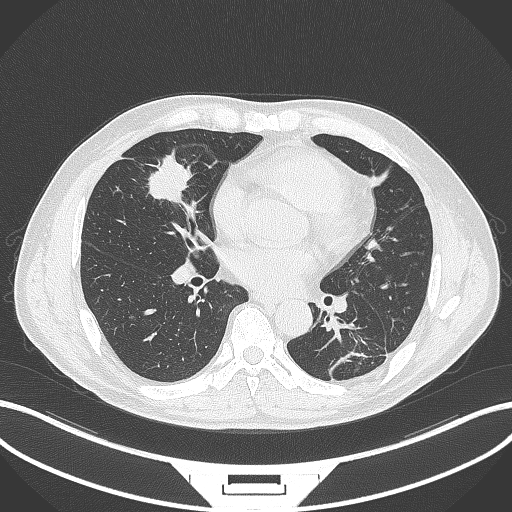
Chest CT, one axial slice; 120 kVp; lung window (W 1500 / L -600 HU); 1 mm slice thickness; 512 × 512 image matrix. Patient: male, 59 years. From the clinical record (not read from this slice): clinical TNM (as recorded): T2a N1 M0.
Outlined on this slice (bounding box drawn by a radiologist):
- lung tumour (recorded histology: adenocarcinoma): bounding box (x1, y1, x2, y2) in pixels: (140, 150, 197, 204)